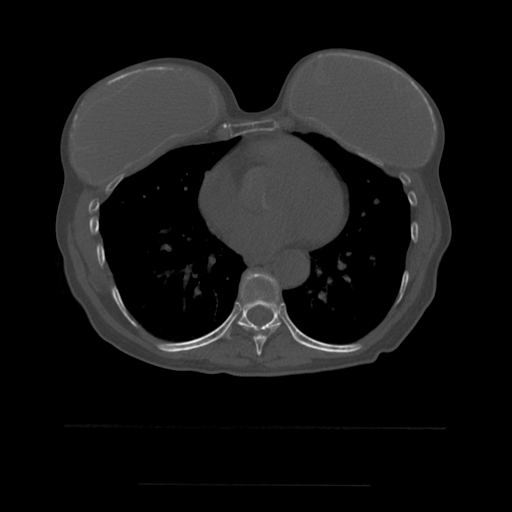
CT including the spine, one axial slice. Position 330 of 544 along the scan axis. Bone window (W 1800 / L 400 HU). 512 × 512 image matrix. Patient age 58 years. From the clinical record (not read from this slice): primary cancer: lung.
Structures marked on this image (semi-automatically segmented with operator editing):
- T8 vertebra: bounding box <240,272,282,356> (left, top, right, bottom; pixels)
- T9 vertebra: <217,273,282,339>